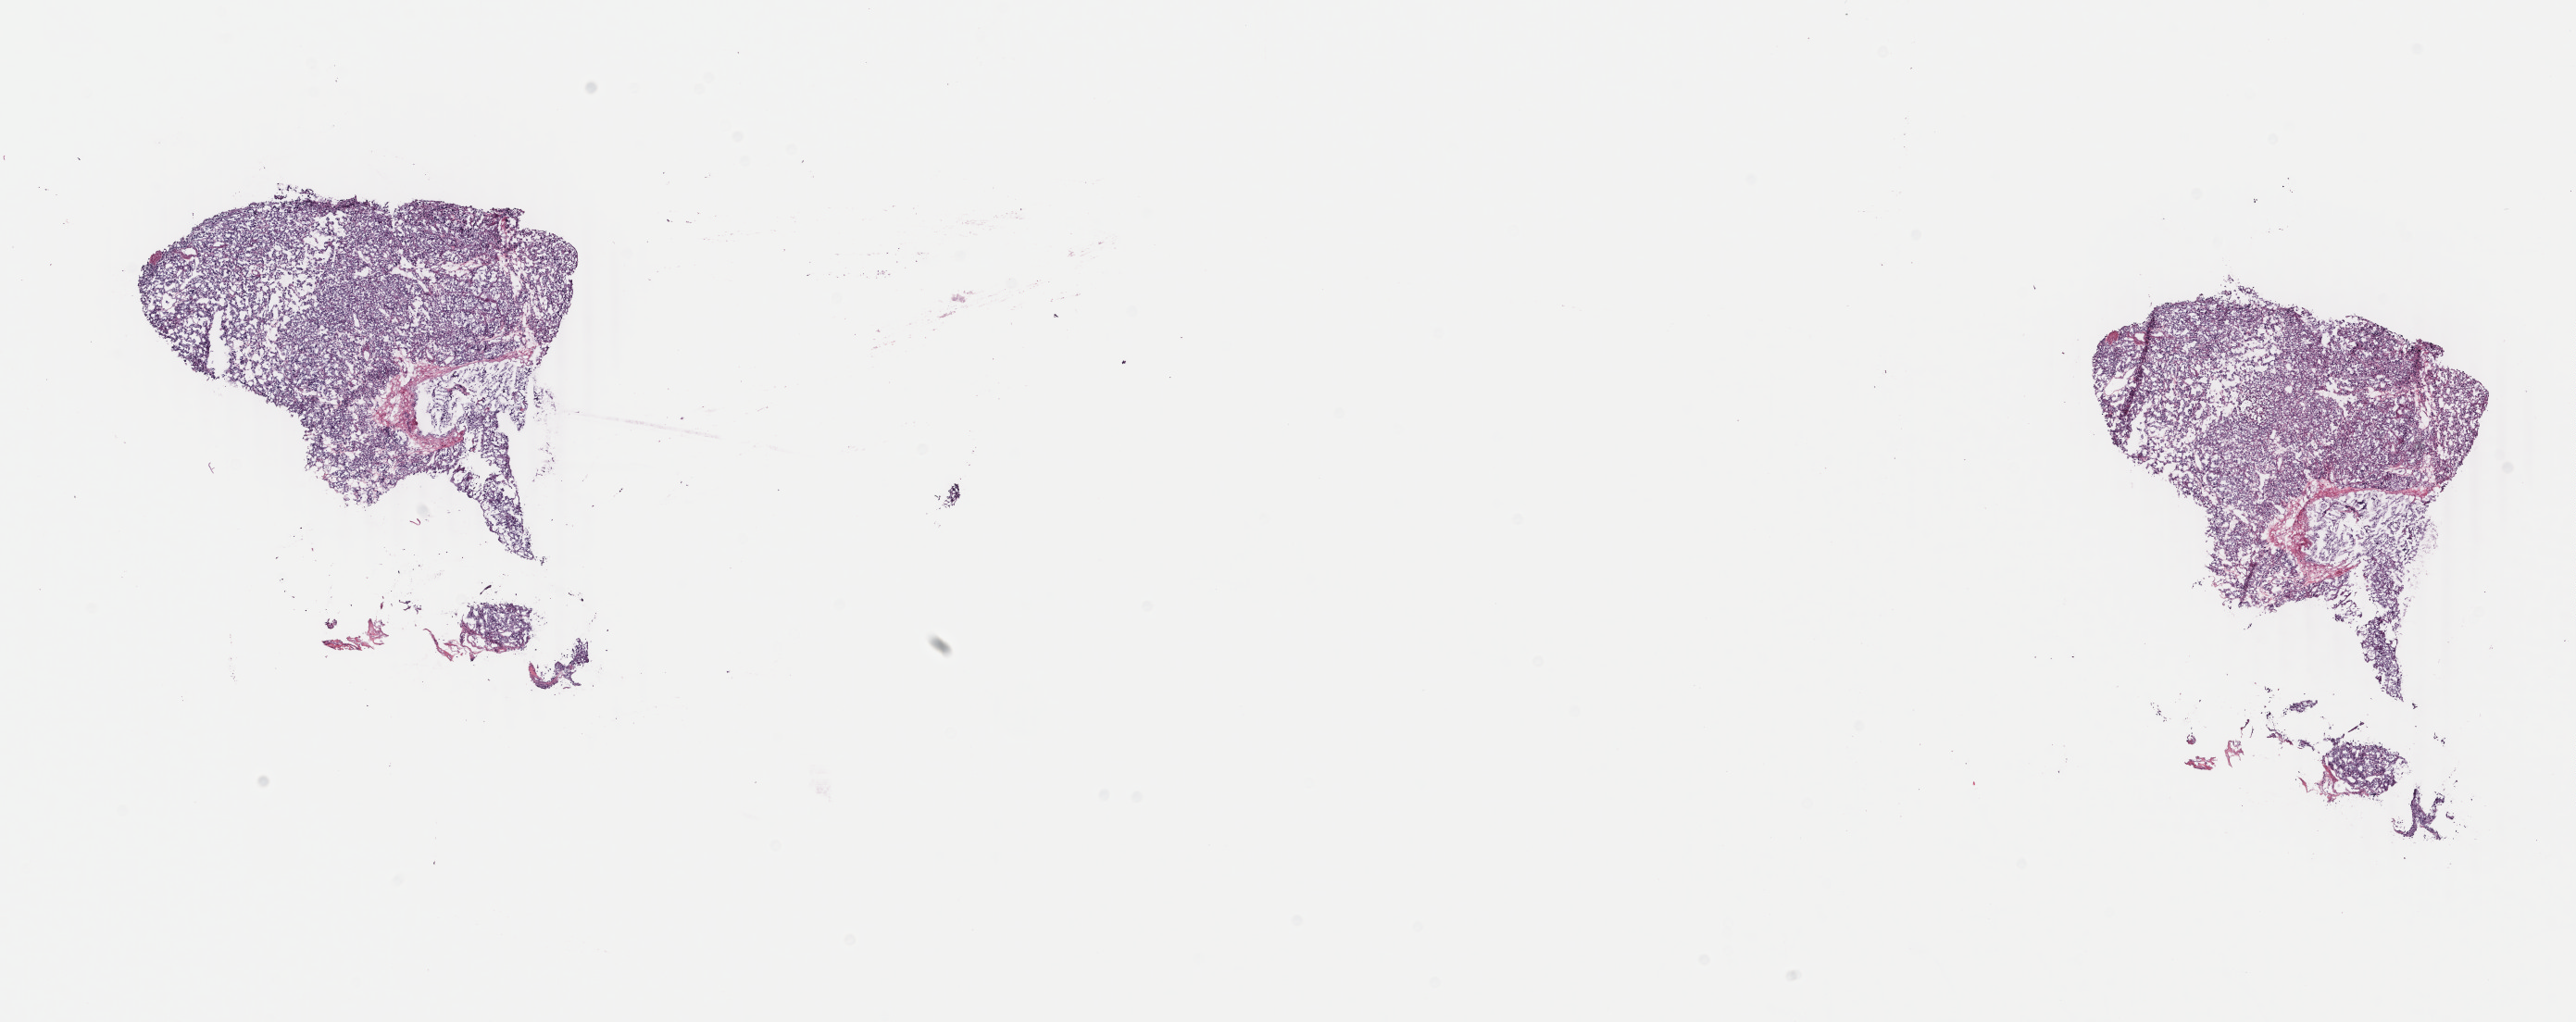
Whole-slide histology image, H&E — shown as a low-resolution overview of the whole scanned area (about 22.1 x 8.8 mm, slide scanned at 40x); frozen section; primary tumour sample from the connective, subcutaneous and other soft tissues. Male, age 27 years at initial diagnosis. Pathologist review of this section (percent, as recorded): tumour cells 100%, tumour nuclei 80%, normal cells 0%, stromal cells 0%, necrosis 0%. Infiltration values recorded for this section: lymphocyte infiltration 1%, monocyte infiltration 0%, neutrophil infiltration 0%.
• histologic diagnosis: Extra-adrenal paraganglioma, NOS (connective, subcutaneous and other soft tissues of trunk, NOS)